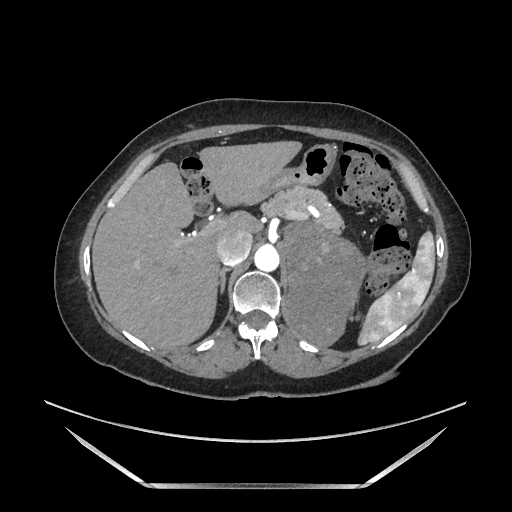
Contrast-enhanced abdominal CT, one axial slice; slice 122 of 205 in the series (ordered by position); soft-tissue window (W 400 / L 40 HU); 512 × 512 image matrix, field of view 440 × 440 mm. Female patient. From the clinical record (not read from this slice): diagnosis: adrenocortical carcinoma; tumour side: left adrenal; tumour size at pathology: 12.5 cm; Ki-67 index: 39 %.
Outlined on this slice (semi-automatic segmentation, software-assisted and operator-edited):
- mass: bounding box <287,222,366,344> (left, top, right, bottom; pixels)